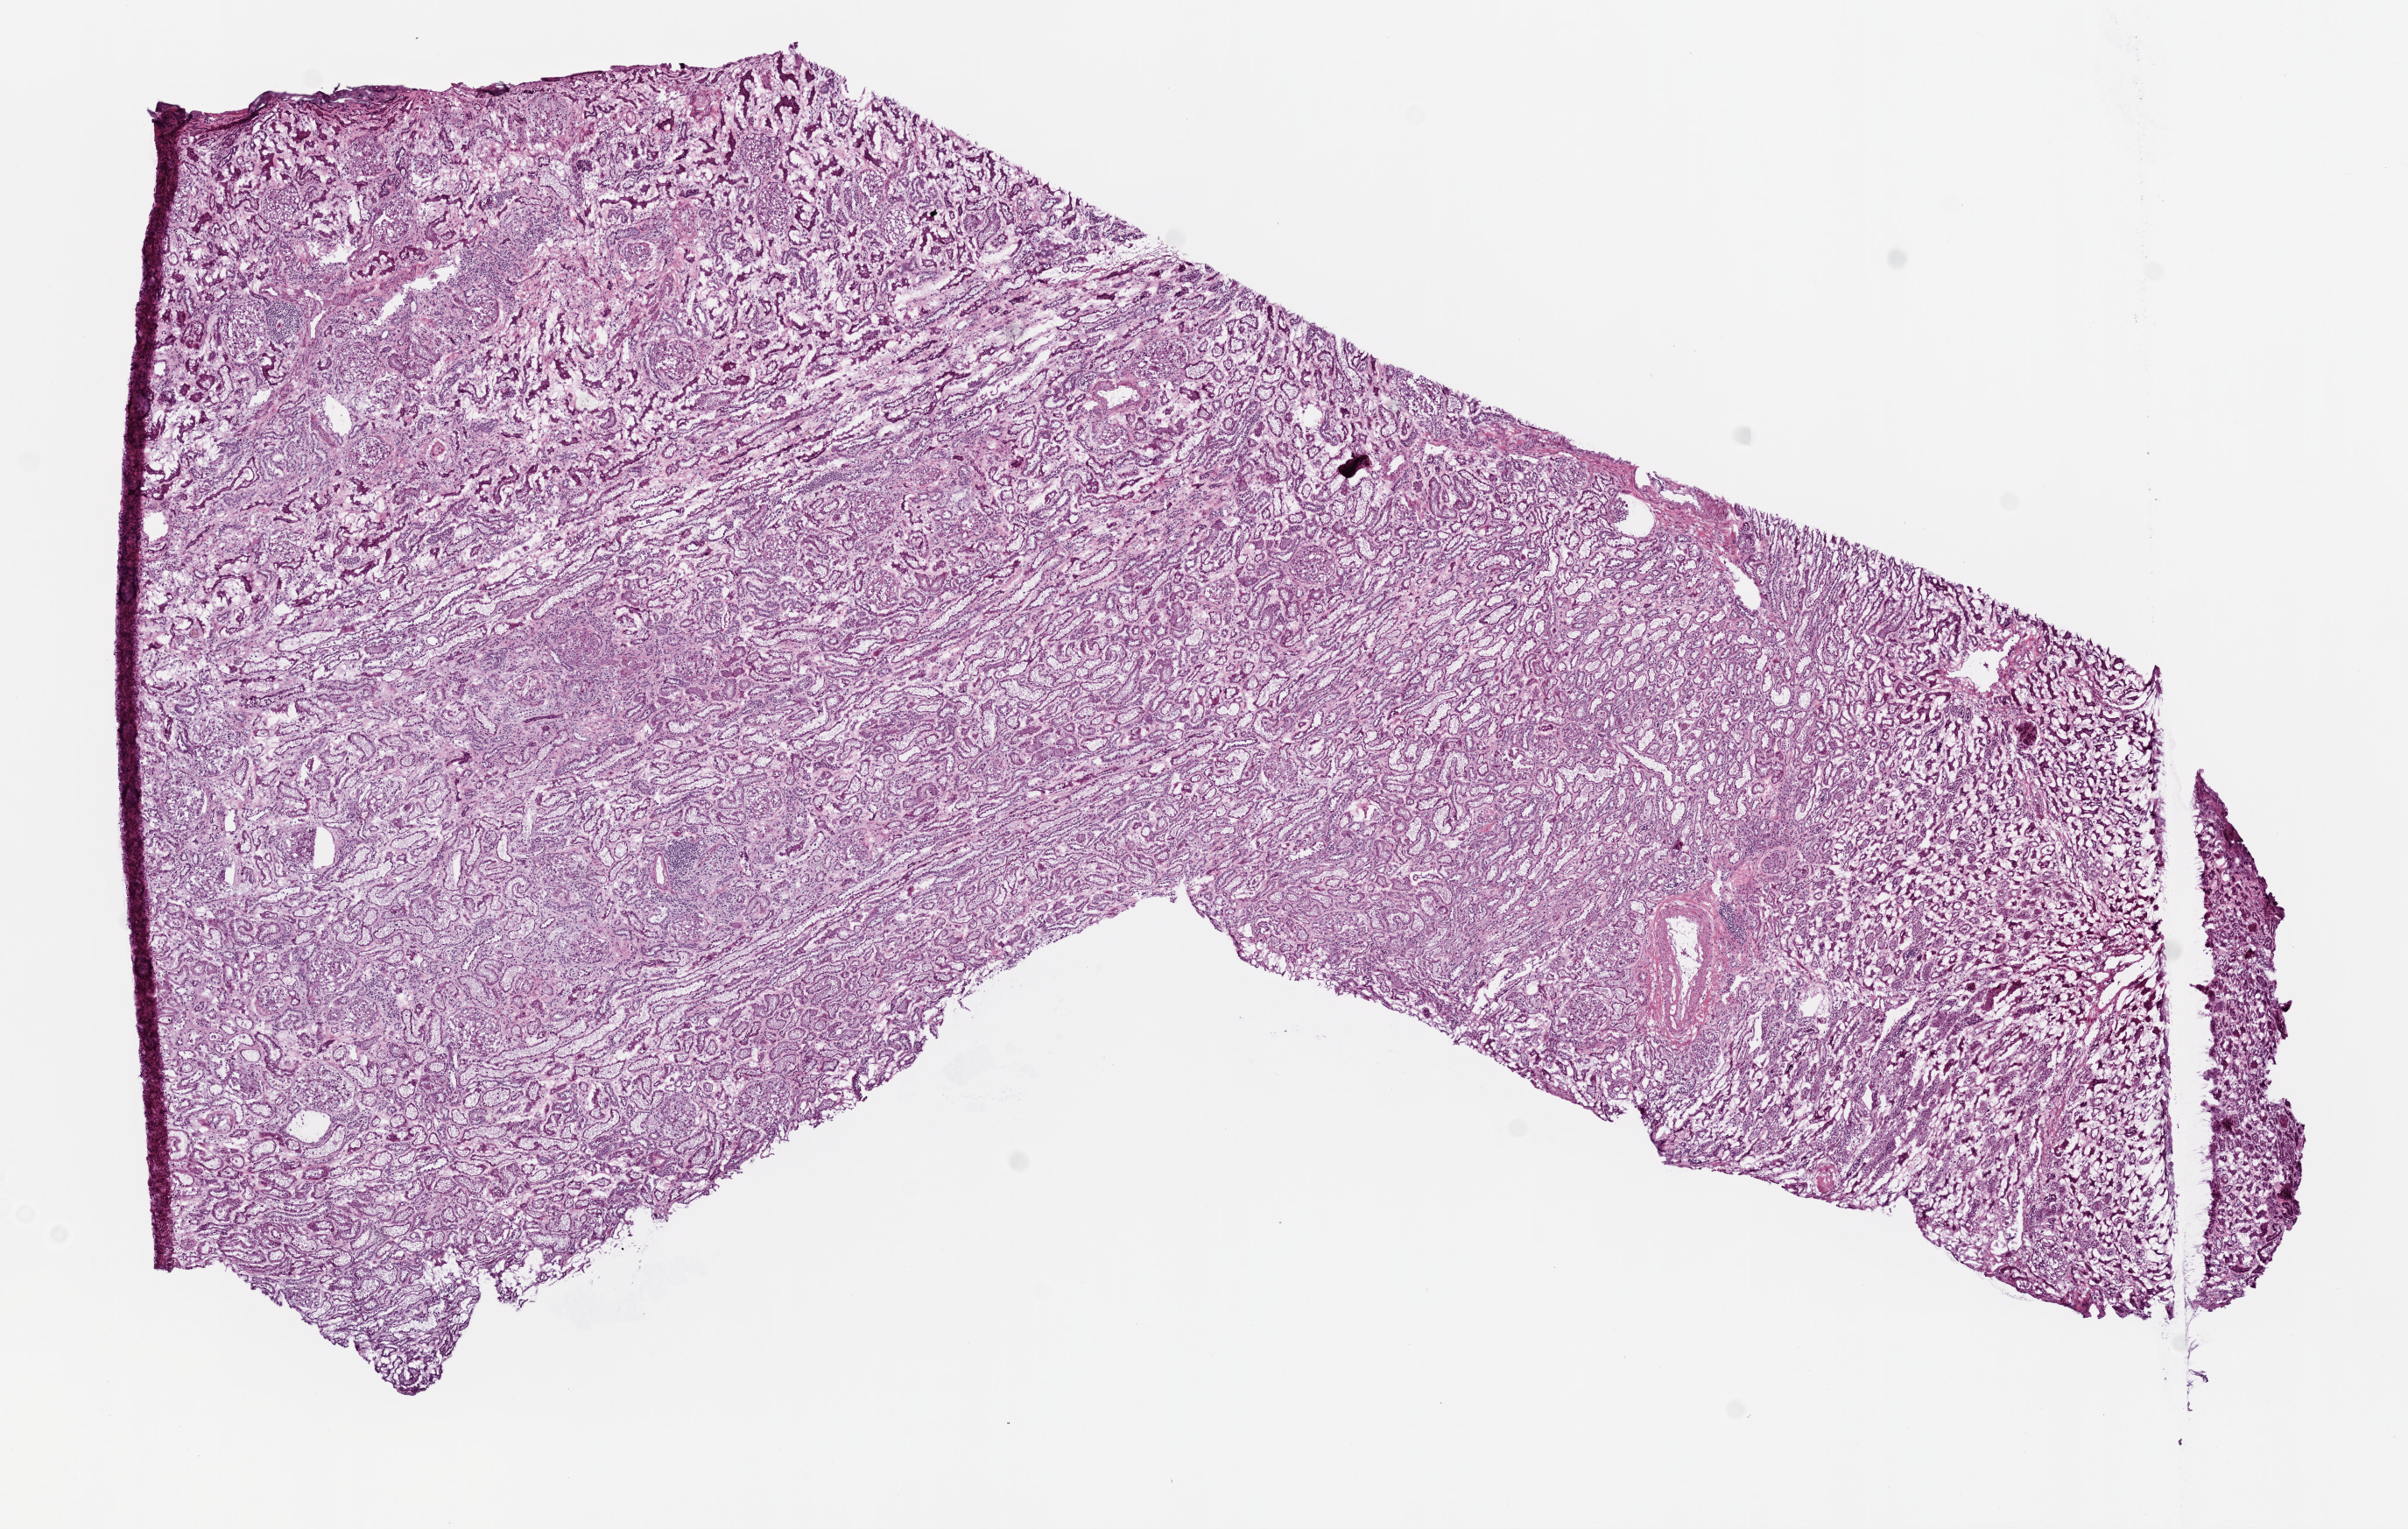
Digitized H&E tissue section (whole slide), whole scanned area (about 11.0 x 7.0 mm, acquisition: 20x scan) shown as a low-resolution overview; frozen section from the top of the tissue portion; kidney, solid tissue normal (non-tumour tissue) sample. Patient: male, age at initial diagnosis 52 years.
This section: solid tissue normal (non-tumour) sample from the same patient. Patient diagnosis: Clear cell adenocarcinoma, NOS.